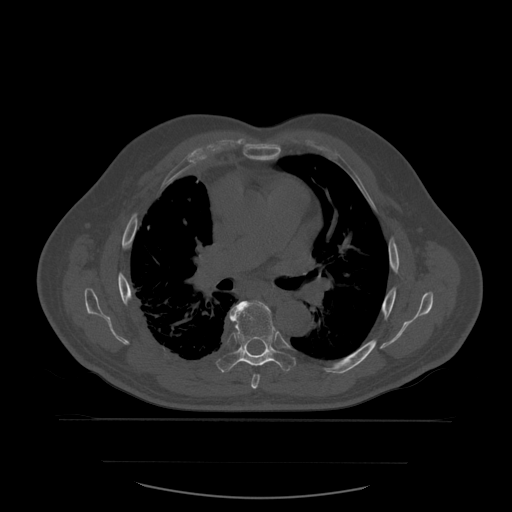
CT including the spine, one axial slice. Position 388 of 590 along the scan axis. Bone window (W 1800 / L 400 HU). 1.25 mm slice thickness. 512 × 512 image matrix, field of view 479 × 479 mm. Patient age 71 years. From the clinical record (not read from this slice): primary cancer: lung; vertebrae with lytic lesions (as recorded): T1, T2, L5, S1.
Outlined on this slice (semi-automatic segmentation, software-assisted and operator-edited):
- T6 vertebra: bounding box [x1, y1, x2, y2] px = [246, 301, 261, 389]
- T7 vertebra: [216, 301, 296, 373]